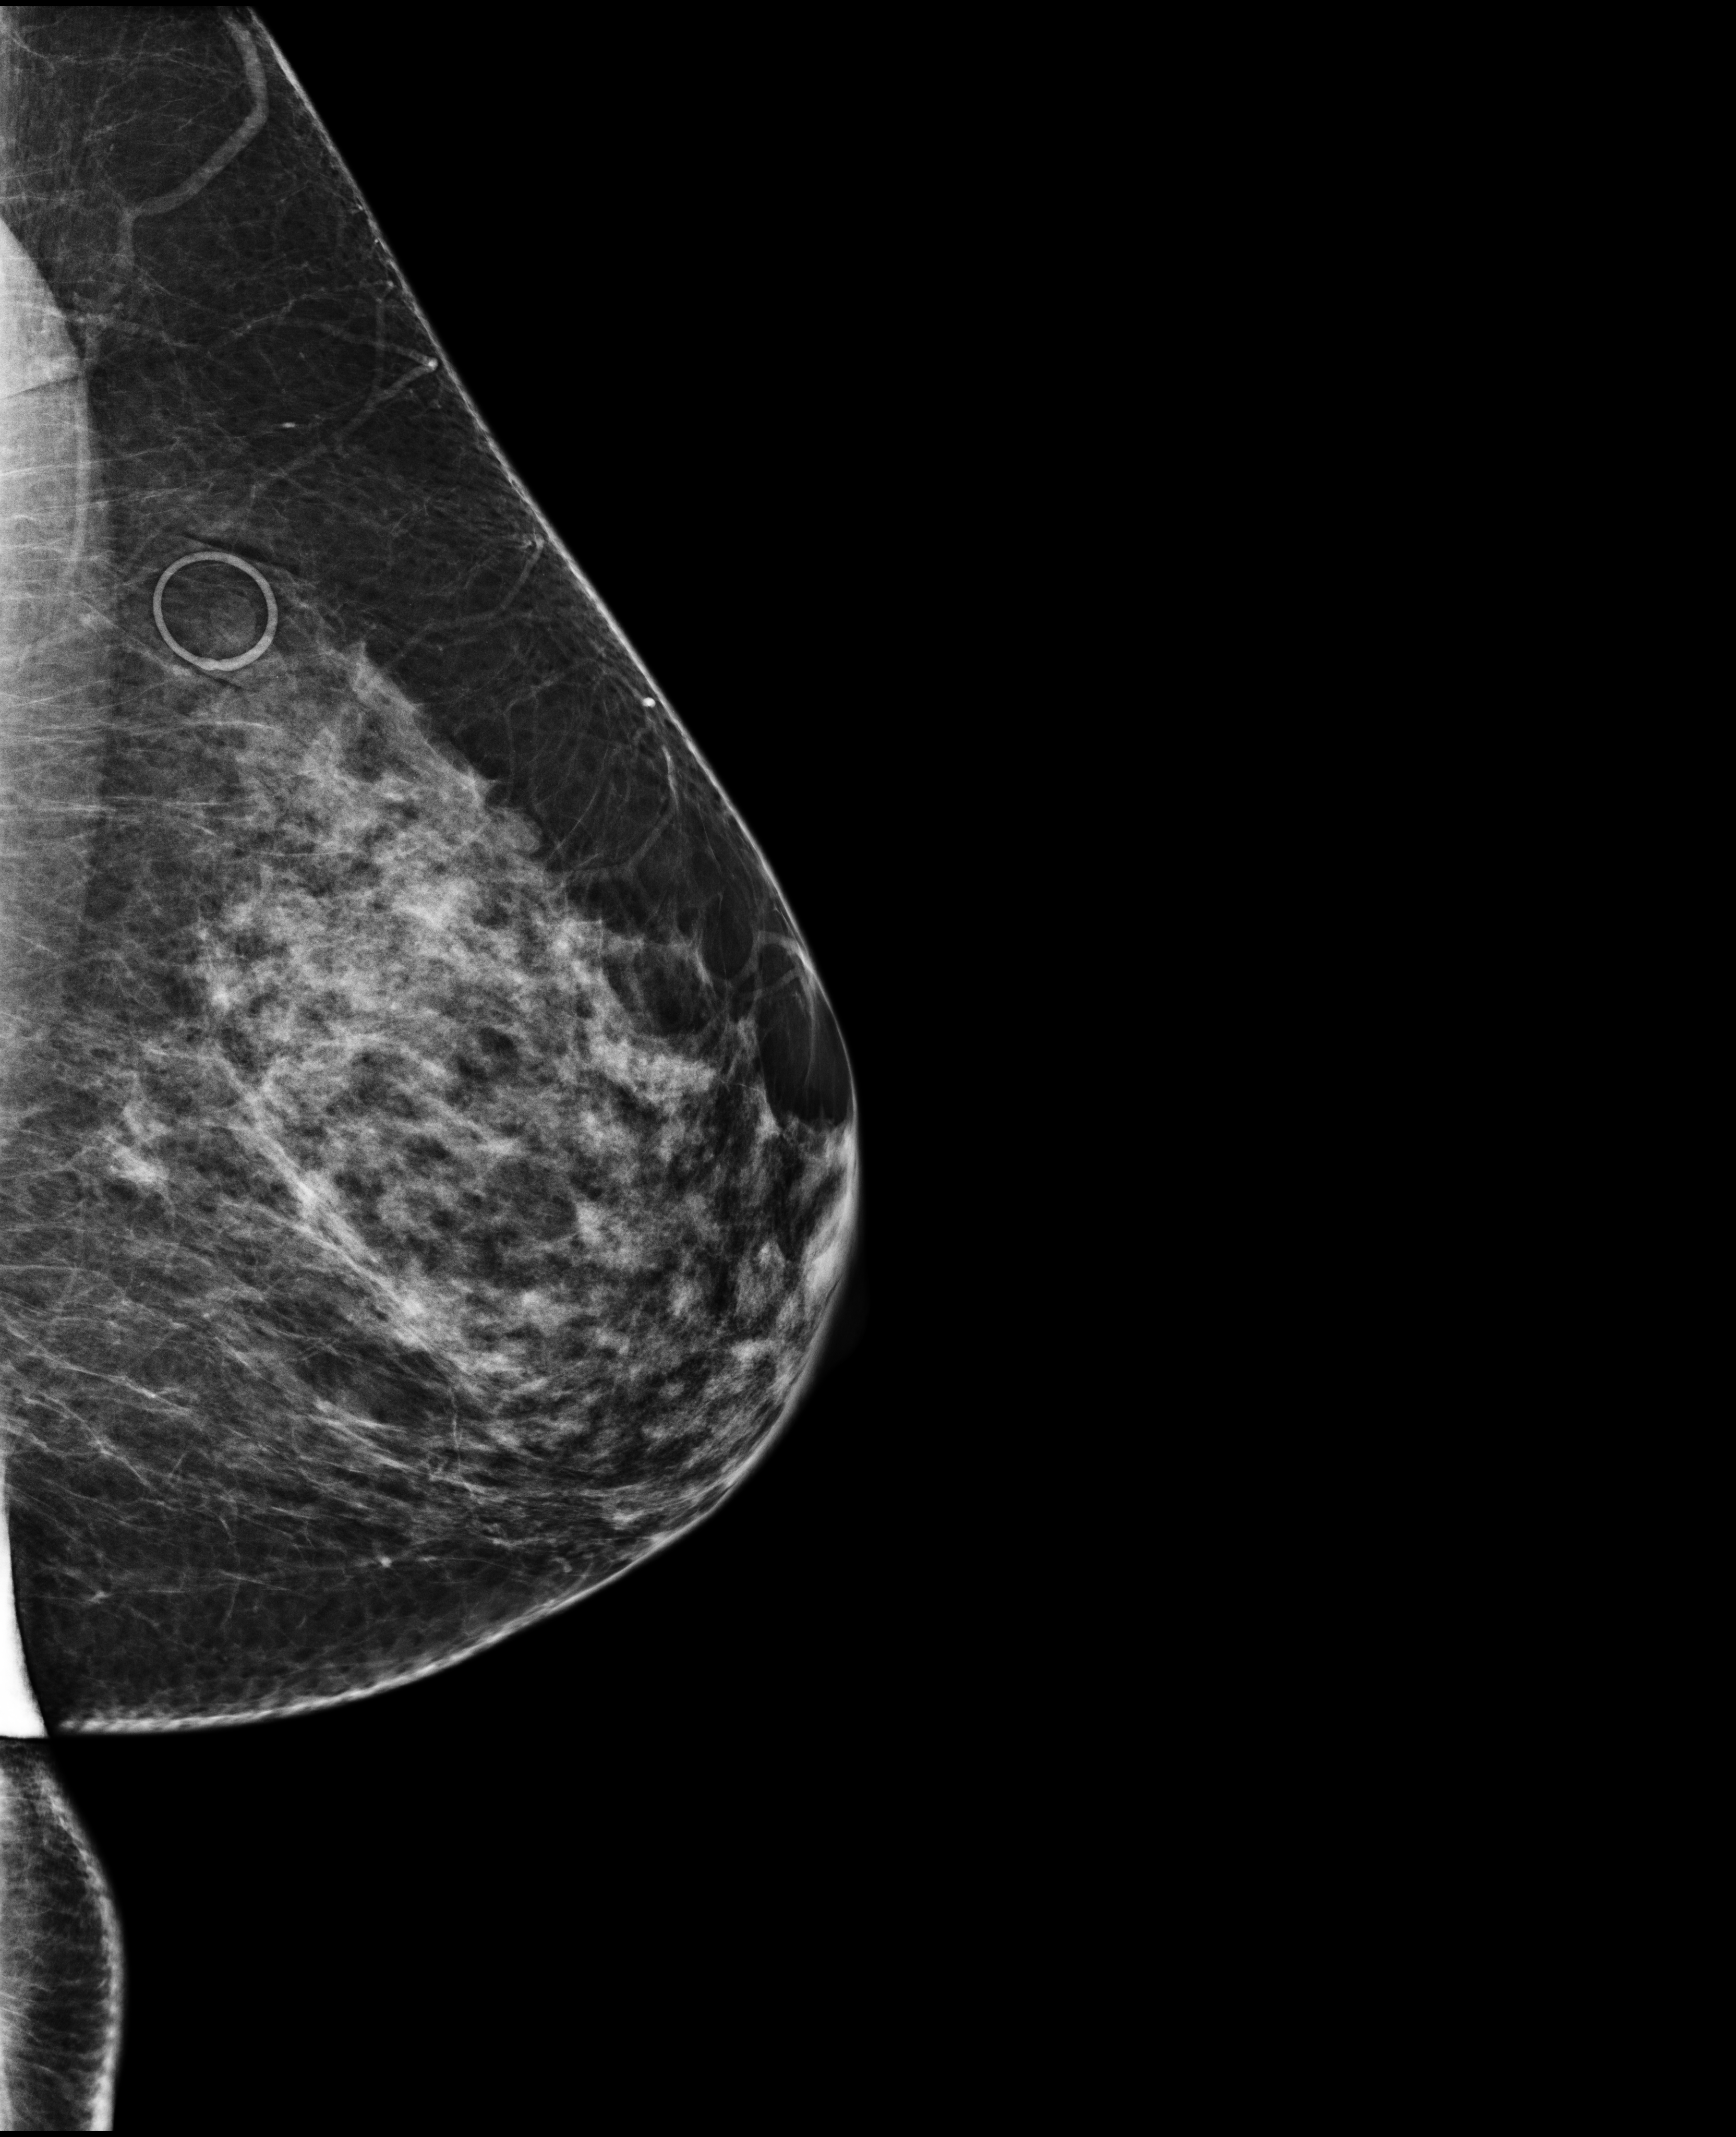
Screening examination; system: Selenia Dimensions. Female patient, age 53 years.
Image type: full-field digital mammogram. Breast: left. Projection: medio-lateral oblique projection.